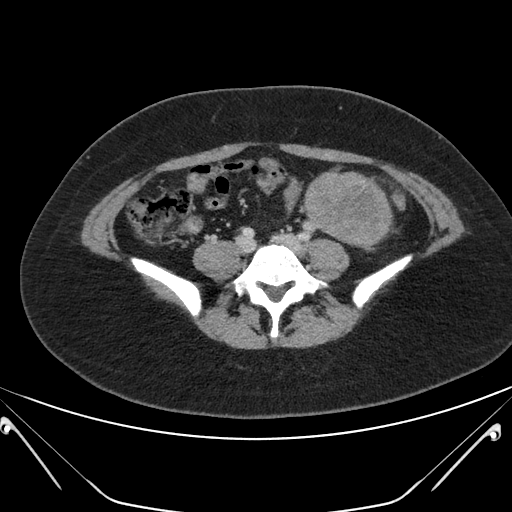
Contrast-enhanced abdominal CT, one axial slice; position 68 of 168 along the scan axis; intravenous contrast given; soft-tissue window (W 400 / L 40 HU); 3 mm slice thickness; 512 × 512 image matrix, field of view 394 × 394 mm. Female patient, age 26 years. Case-level facts recorded for this patient, not image findings: diagnosis: adrenocortical carcinoma; tumour side: left adrenal; tumour size at pathology: 28 cm; Ki-67 index: 20 %; stage (as recorded): 2.
Annotated regions visible in this slice (semi-automatically segmented with operator editing):
- mass: box from (x=307, y=174) to (x=389, y=244) px